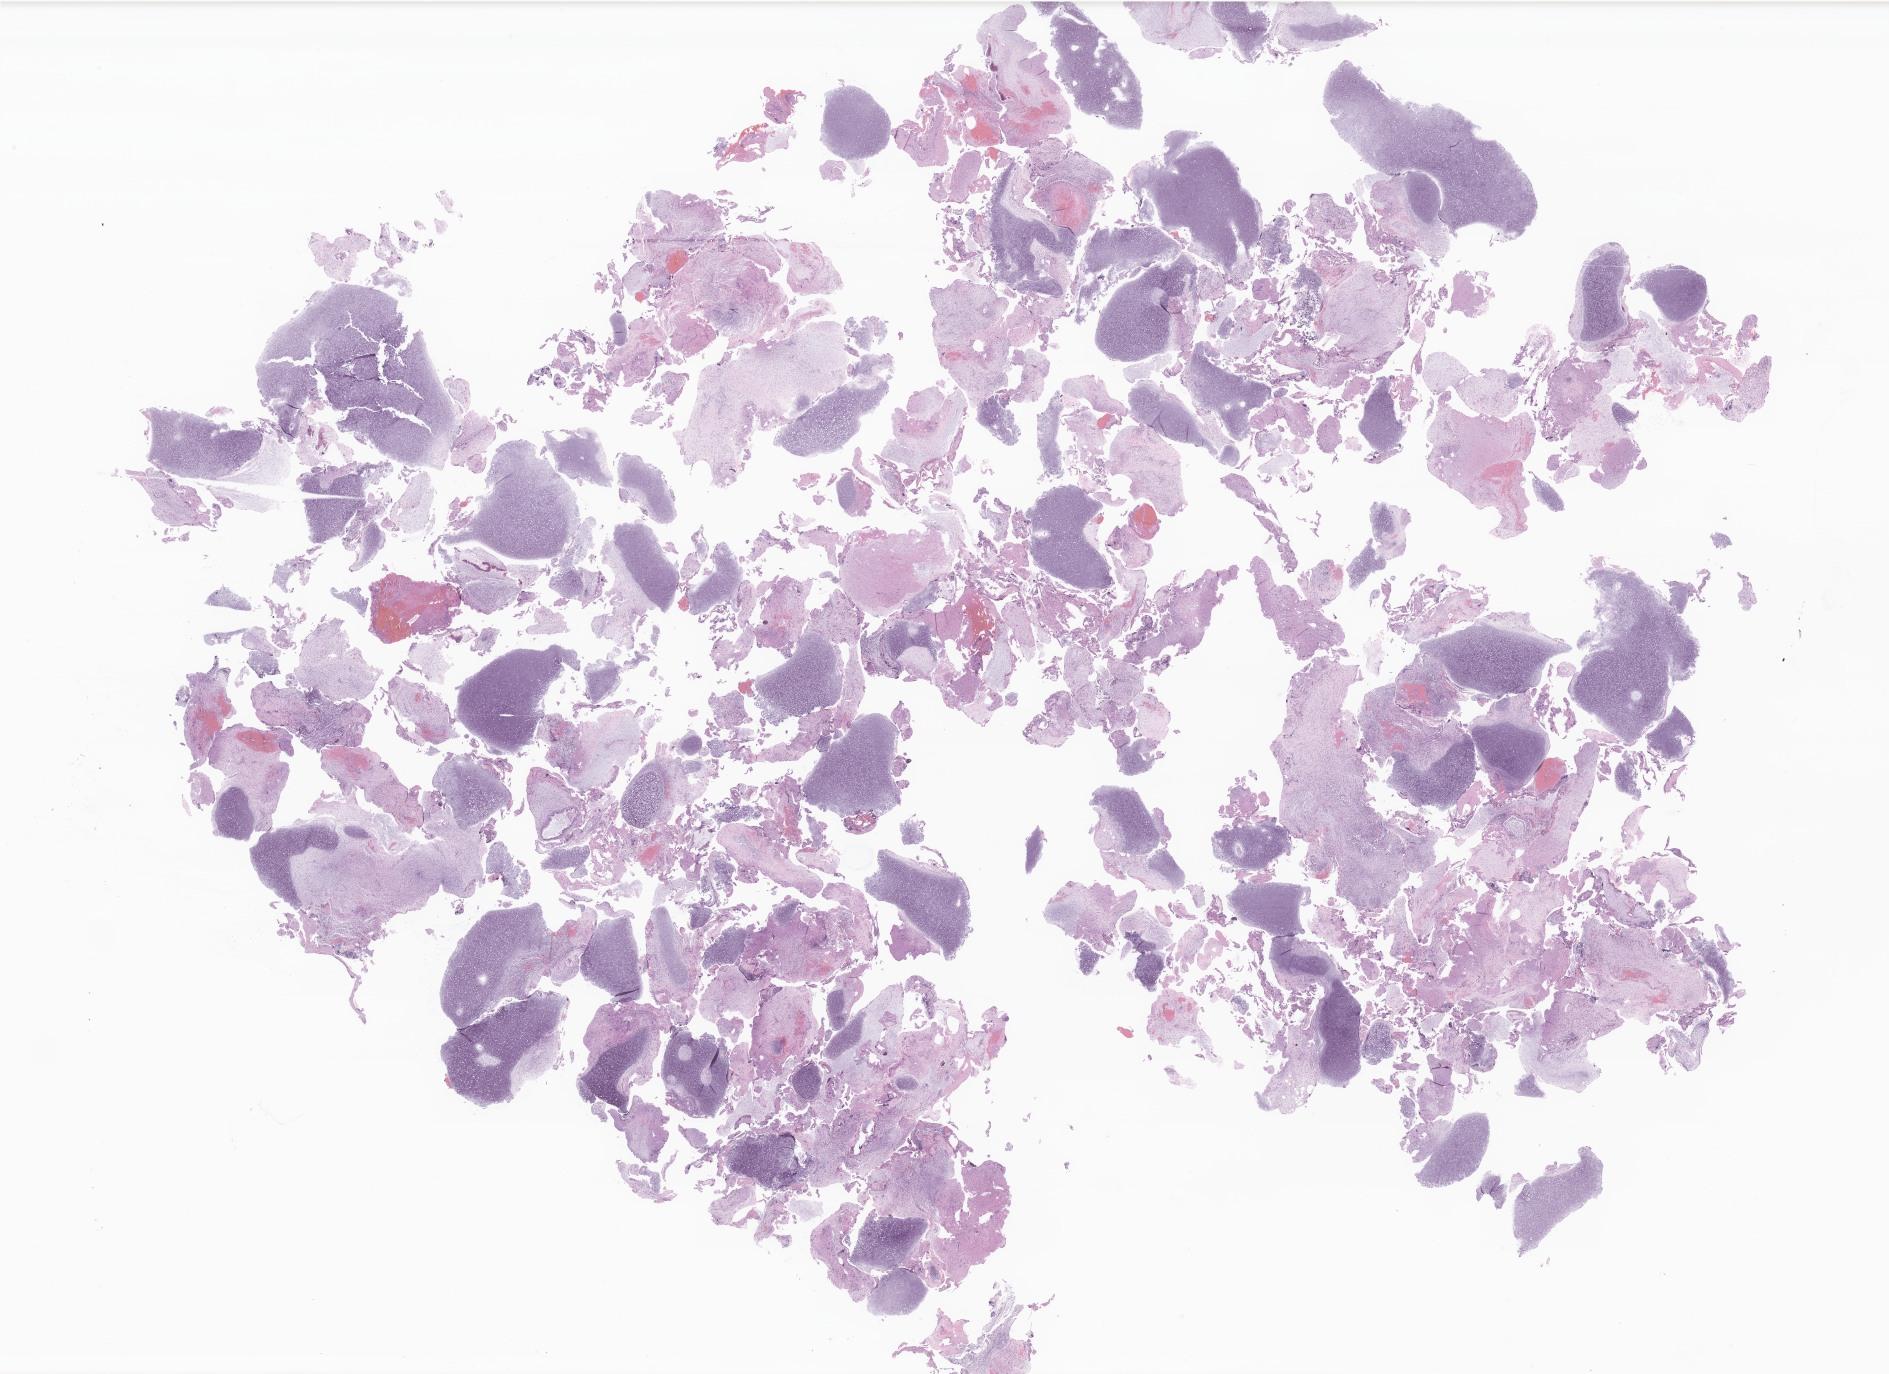
Whole-slide image, H&E stain of tumor tissue from the brain — a low-resolution overview of the entire scanned area, about 31.9 x 23.2 mm; formalin-fixed paraffin-embedded section. Patient: male, age 59 months (4 years 11 months).
* recorded diagnosis: Mixed germ cell tumor